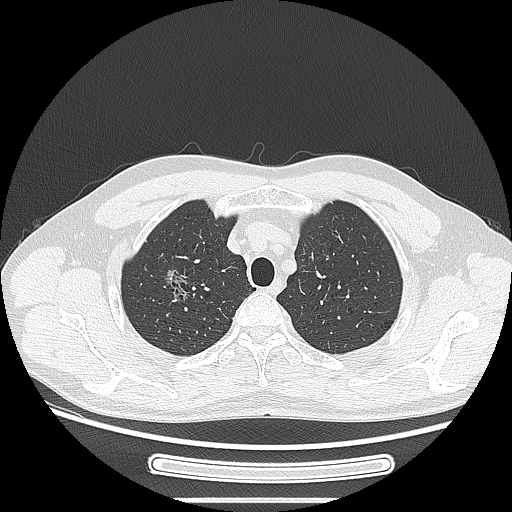
Chest CT, one axial slice. Slice 218 of 269 in the series (ordered by position). 120 kVp. Lung window (W 1500 / L -600 HU). 1.25 mm slice thickness. 512 × 512 image matrix. Male patient, age 53 years. Case-level facts recorded for this patient, not image findings: clinical TNM (as recorded): T1c N0 M0; histopathological grade: G2.
Annotated regions visible in this slice (bounding box drawn by a radiologist):
- lung tumour (recorded histology: adenocarcinoma): bounding box <157,260,198,315> (left, top, right, bottom; pixels)